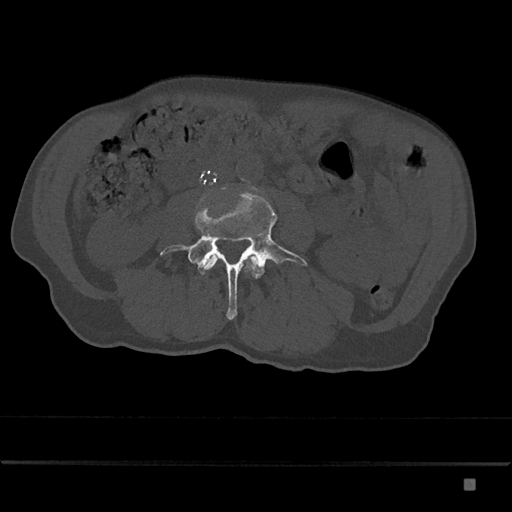
CT including the spine, one axial slice. Slice 354 of 797 in the series (ordered by position). Reconstruction kernel Br40s/3. 120 kVp. Bone window (W 1800 / L 400 HU). 0.5 mm slice thickness. 512 × 512 image matrix, field of view 390 × 390 mm. Patient: male, 72 years. From the clinical record (not read from this slice): primary cancer: prostate.
Annotated regions visible in this slice (semi-automatically segmented with operator editing):
- L3 vertebra: bounding box <204,255,258,270> (left, top, right, bottom; pixels)
- L4 vertebra: <160,192,307,320>